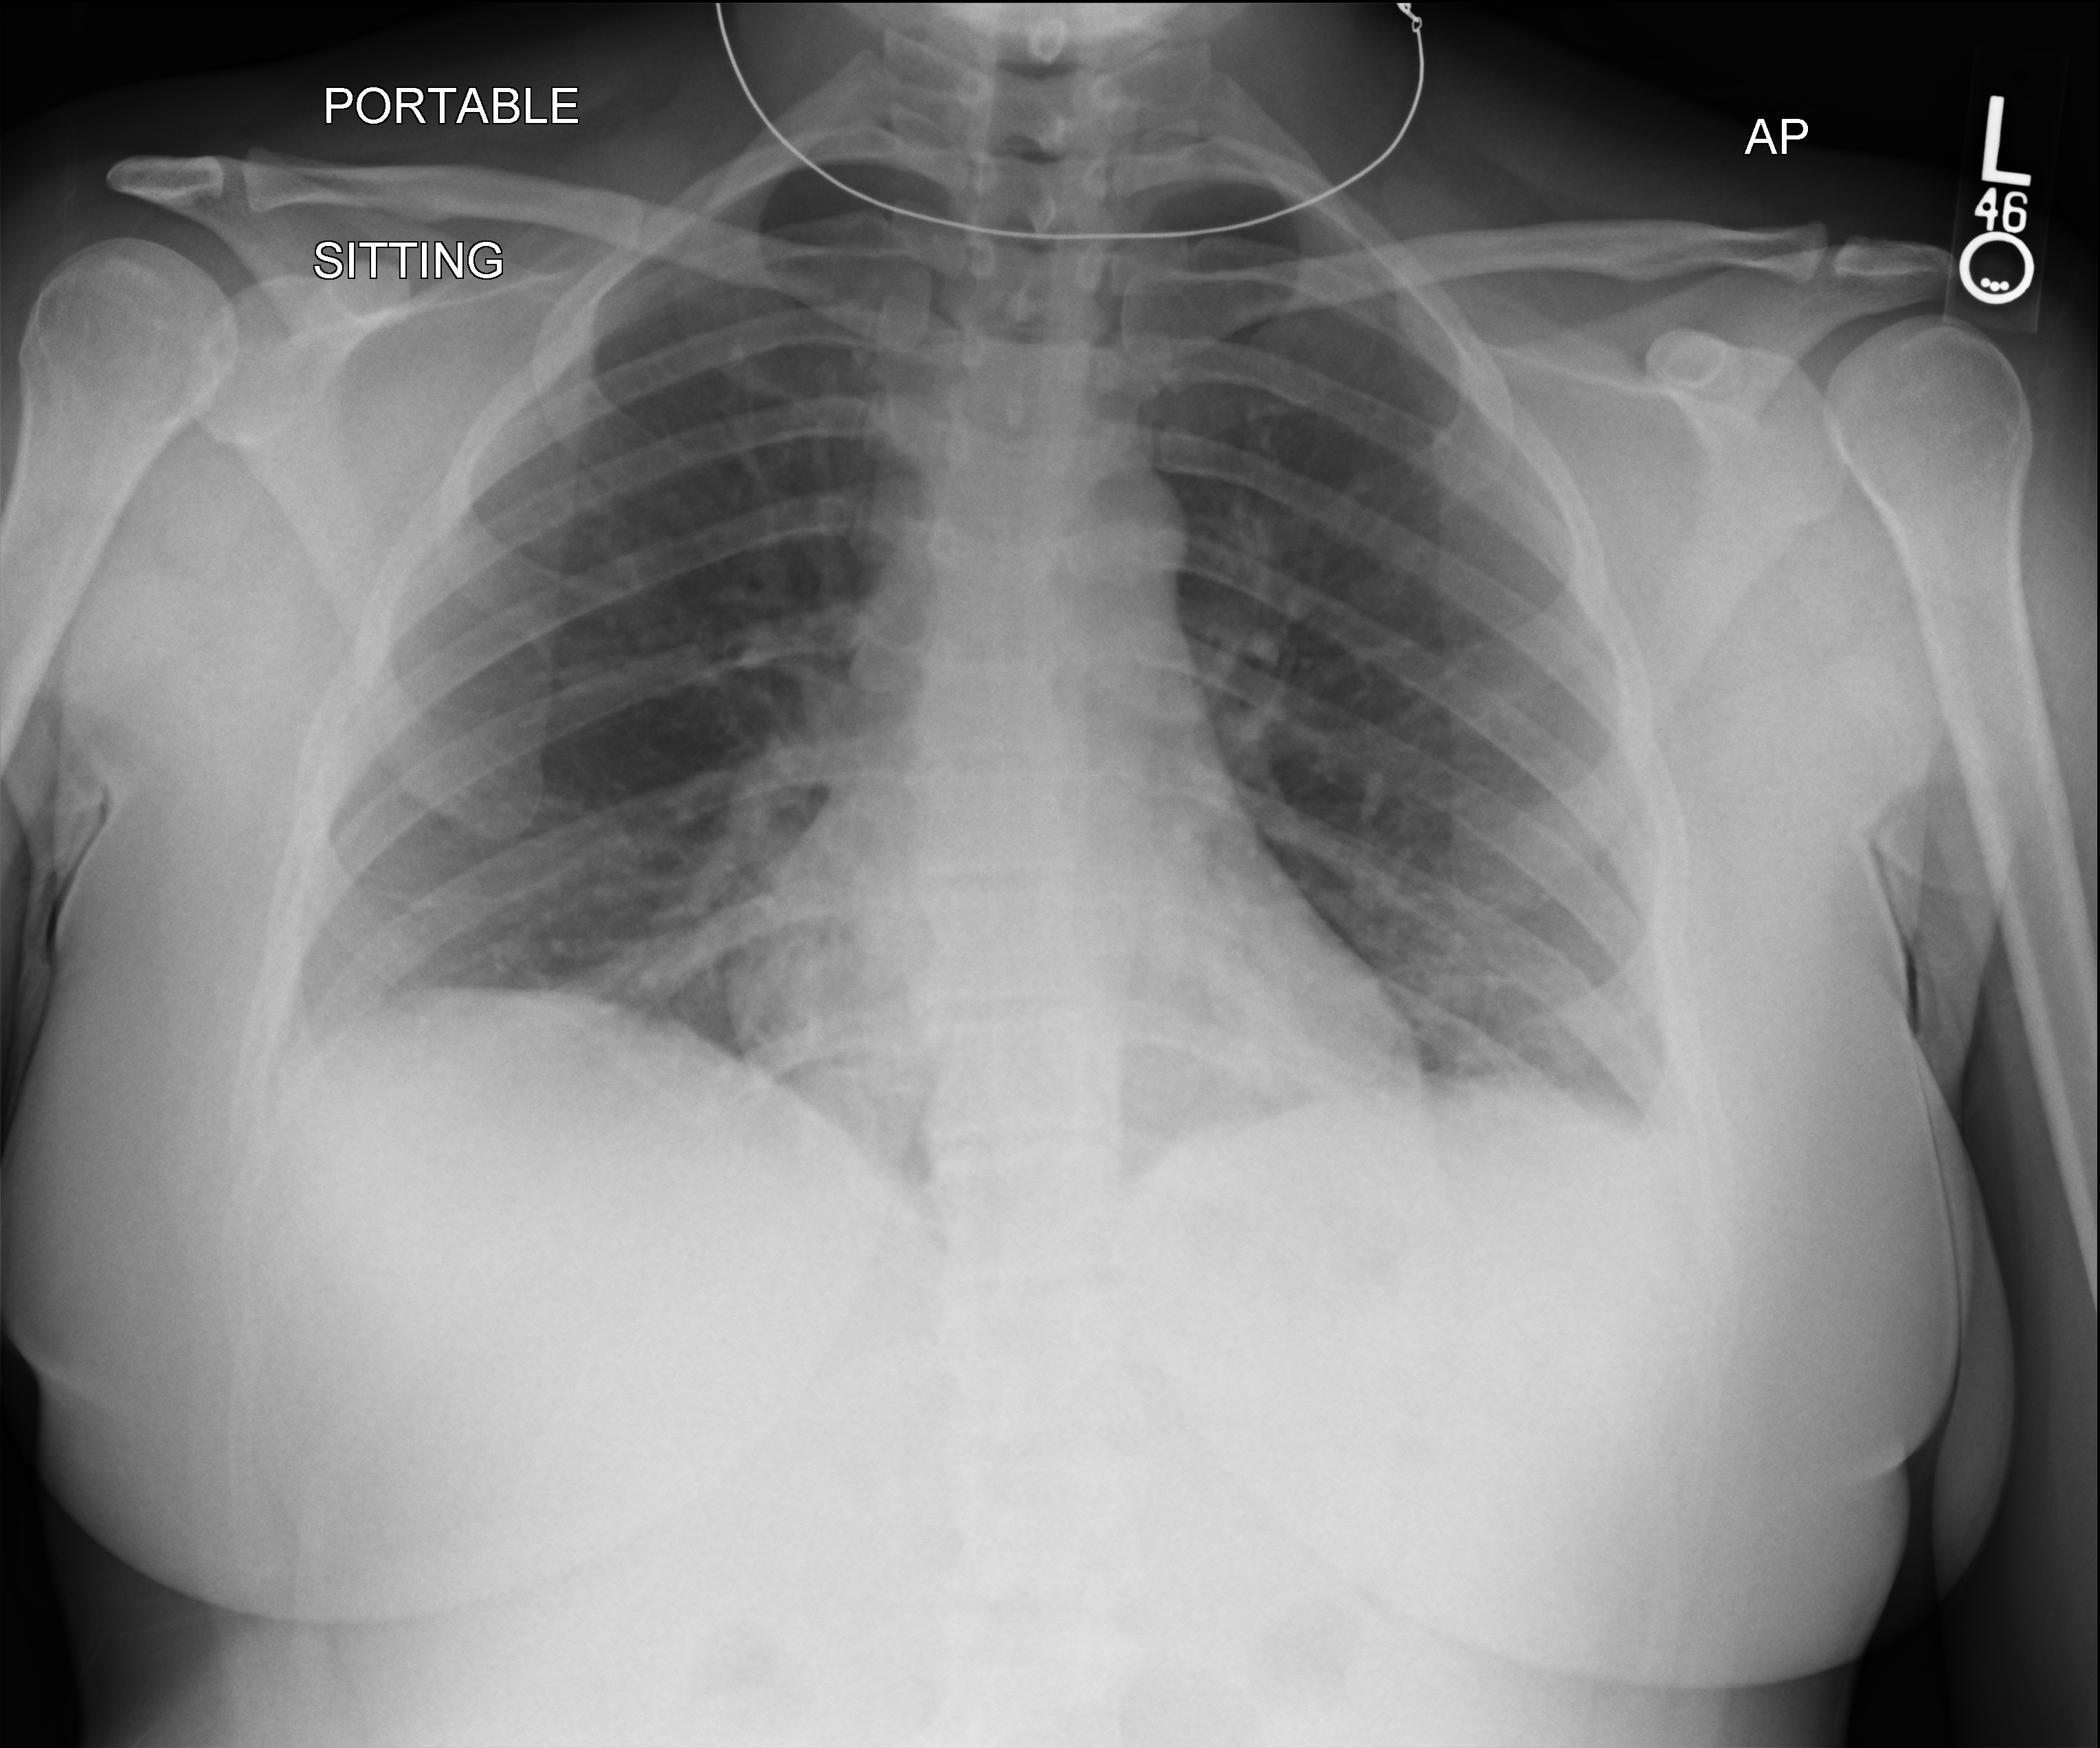
Chest X-ray (portable); anteroposterior (AP) projection. Female patient hospitalised with COVID-19, age 18–59 years.
Hospital-stay facts (about this admission, not read from this image; timing relative to this image not recorded): mechanically ventilated during this hospital stay: no.